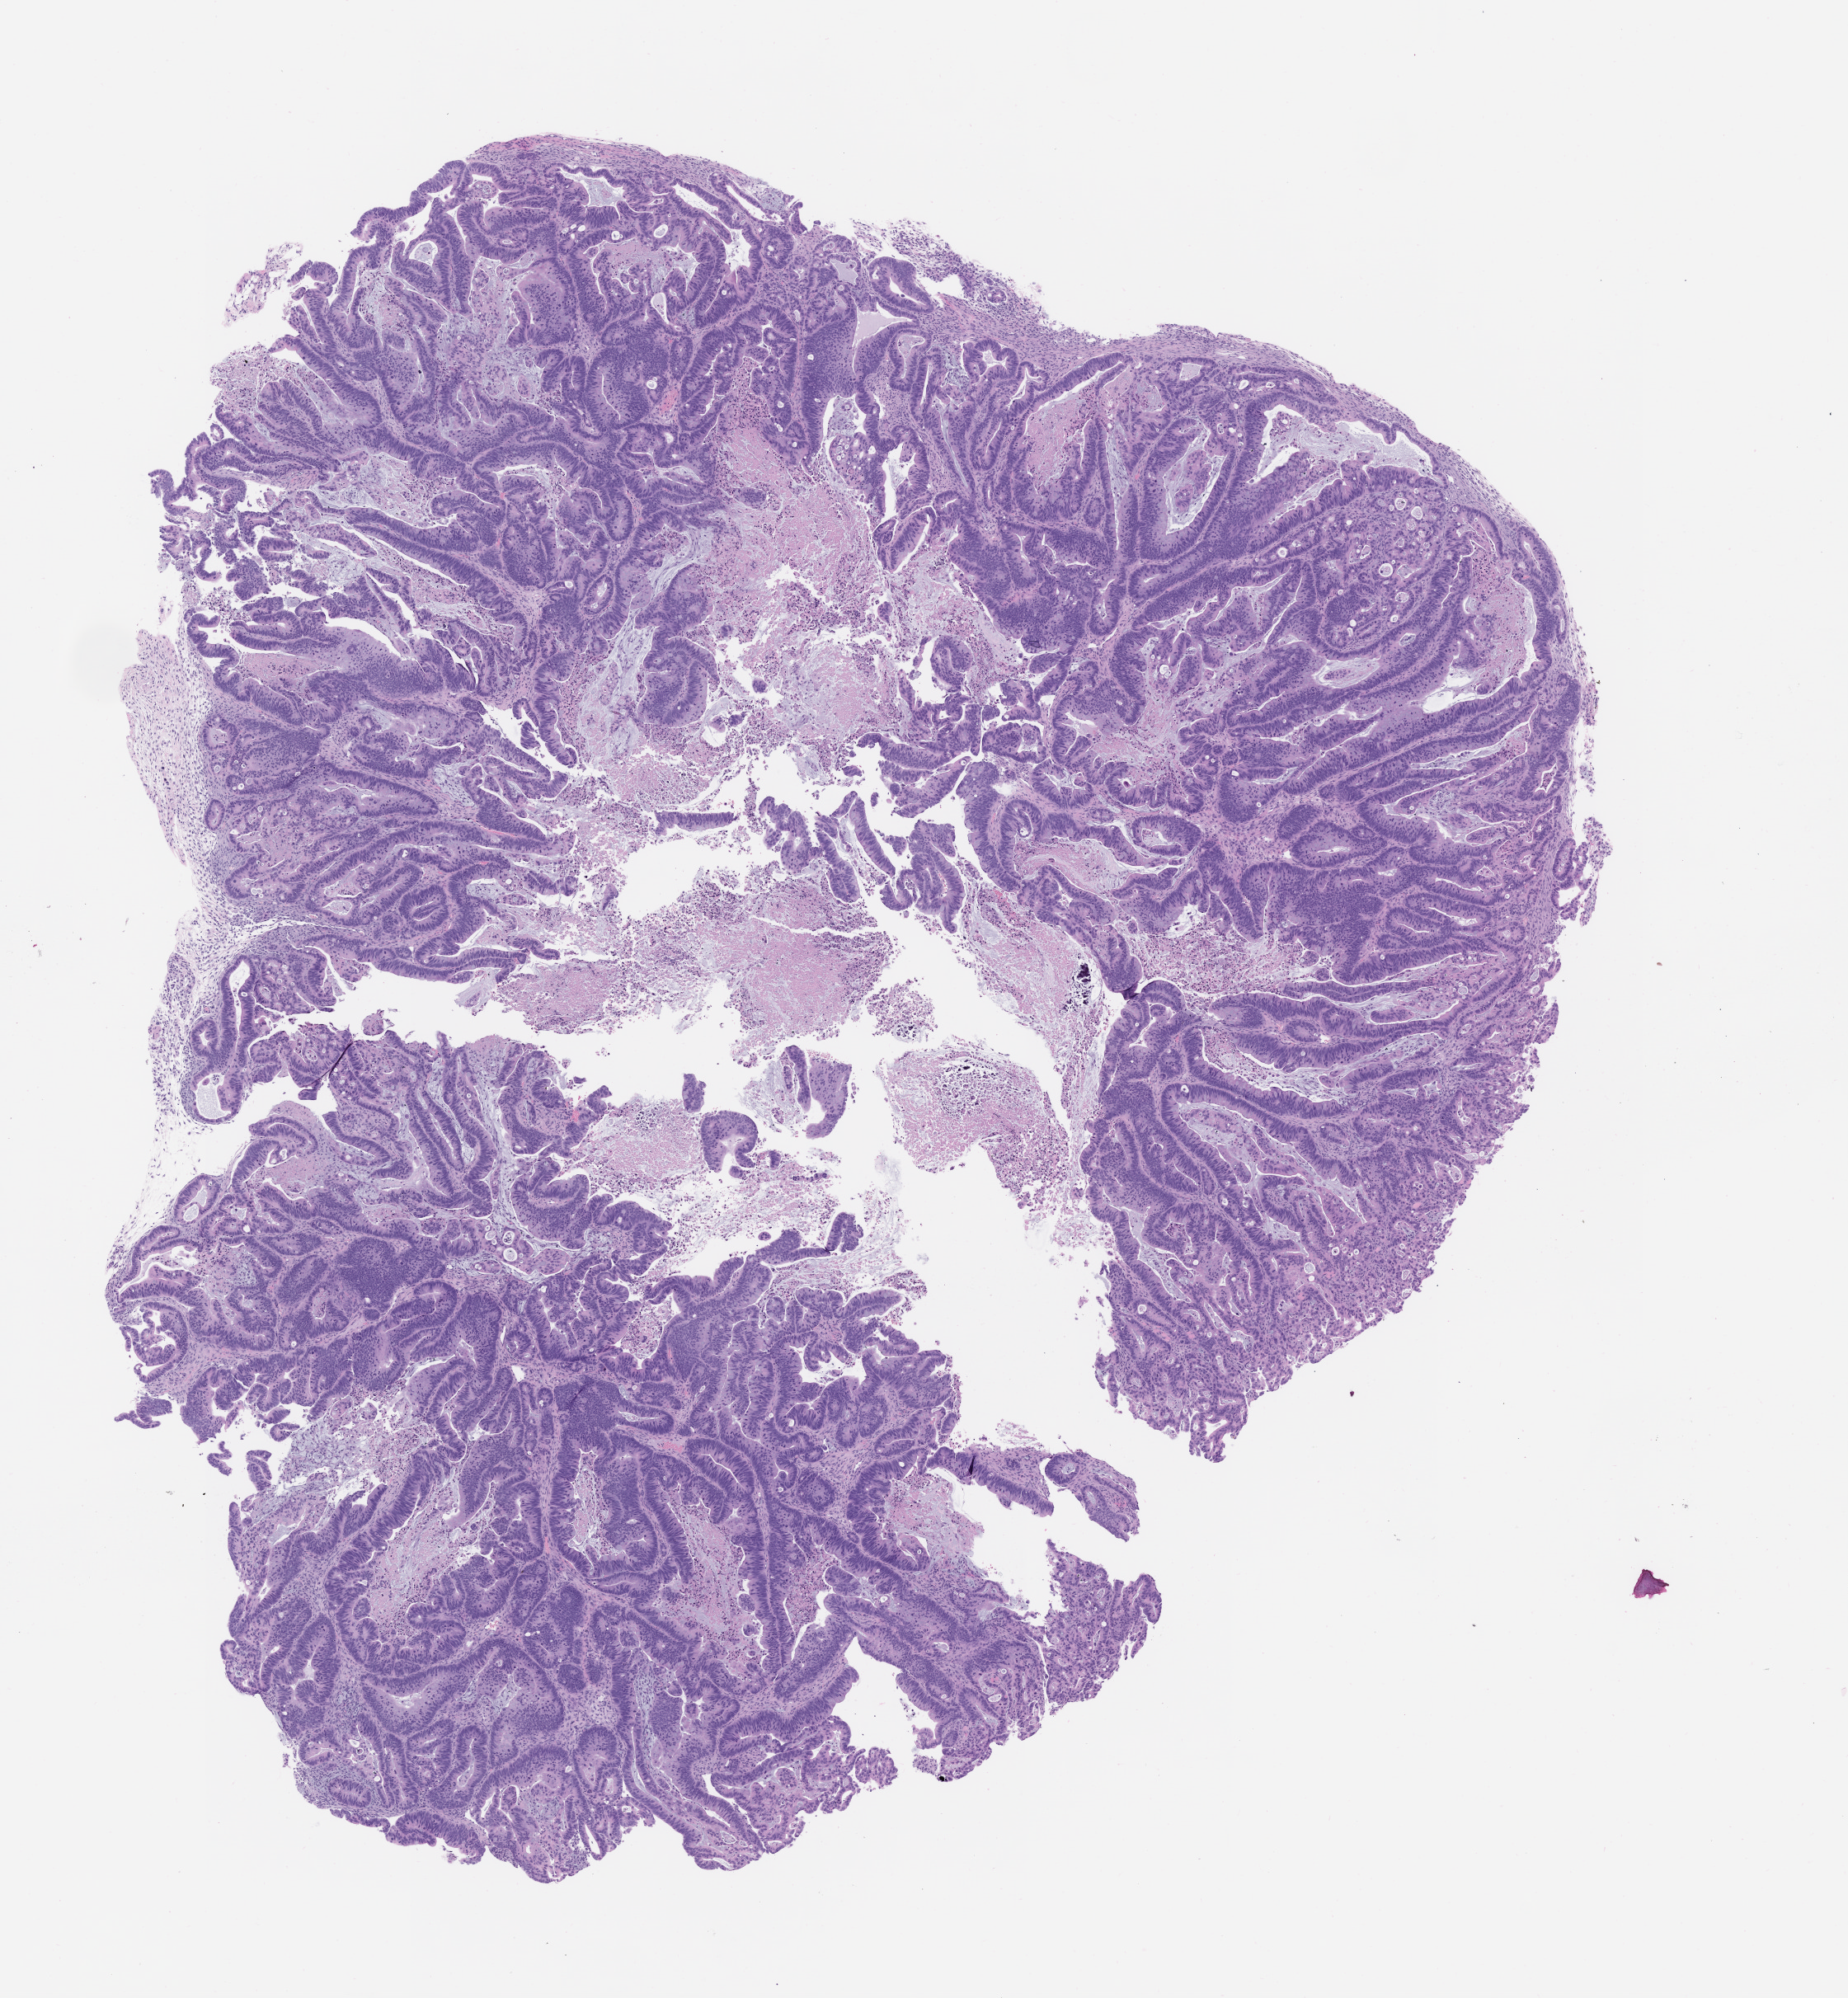
Hematoxylin and eosin (H&E) whole-slide image of a patient-derived xenograft (PDX) tumor grown in a mouse, passage 2 — low-resolution overview of the scanned area, about 9.0 x 9.7 mm, formalin-fixed paraffin-embedded section, originating tumor site category: colon.
* originating patient diagnosis: Colon Adenocarcinoma